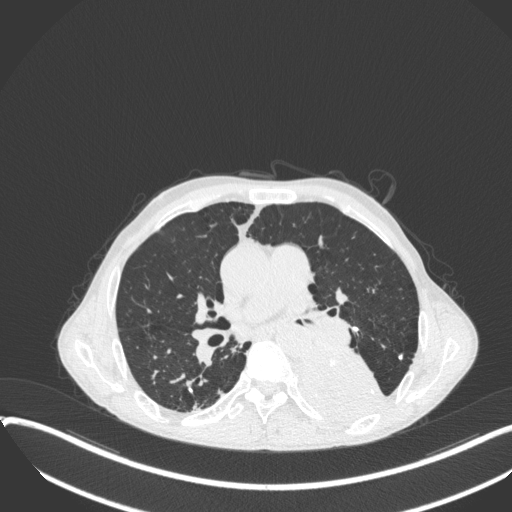
Chest CT, one axial slice; position 209 of 400 along the scan axis; lung window (W 1500 / L -600 HU); 1 mm slice thickness; 512 × 512 image matrix, field of view 400 × 400 mm. Male patient, age 57 years. Case-level facts recorded for this patient, not image findings: clinical TNM (as recorded): T4 N0 M0.
Outlined on this slice (rectangle marked by the reading radiologist):
- lung tumour (recorded histology: squamous cell carcinoma): box from (x=300, y=346) to (x=390, y=427) px